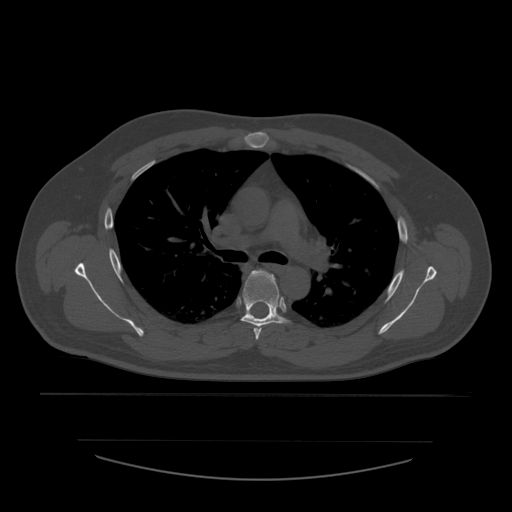
CT including the spine, one axial slice; slice 401 of 532 in the series (ordered by position); 120 kVp; bone window (W 1800 / L 400 HU); 512 × 512 image matrix, field of view 441 × 441 mm. Patient age 44 years. From the clinical record (not read from this slice): primary cancer: soft tissue sarcoma.
Annotated regions visible in this slice (semi-automatic segmentation, software-assisted and operator-edited):
- T4 vertebra: box from (x=254, y=275) to (x=274, y=340) px
- T5 vertebra: (x=241, y=270)–(x=289, y=327)